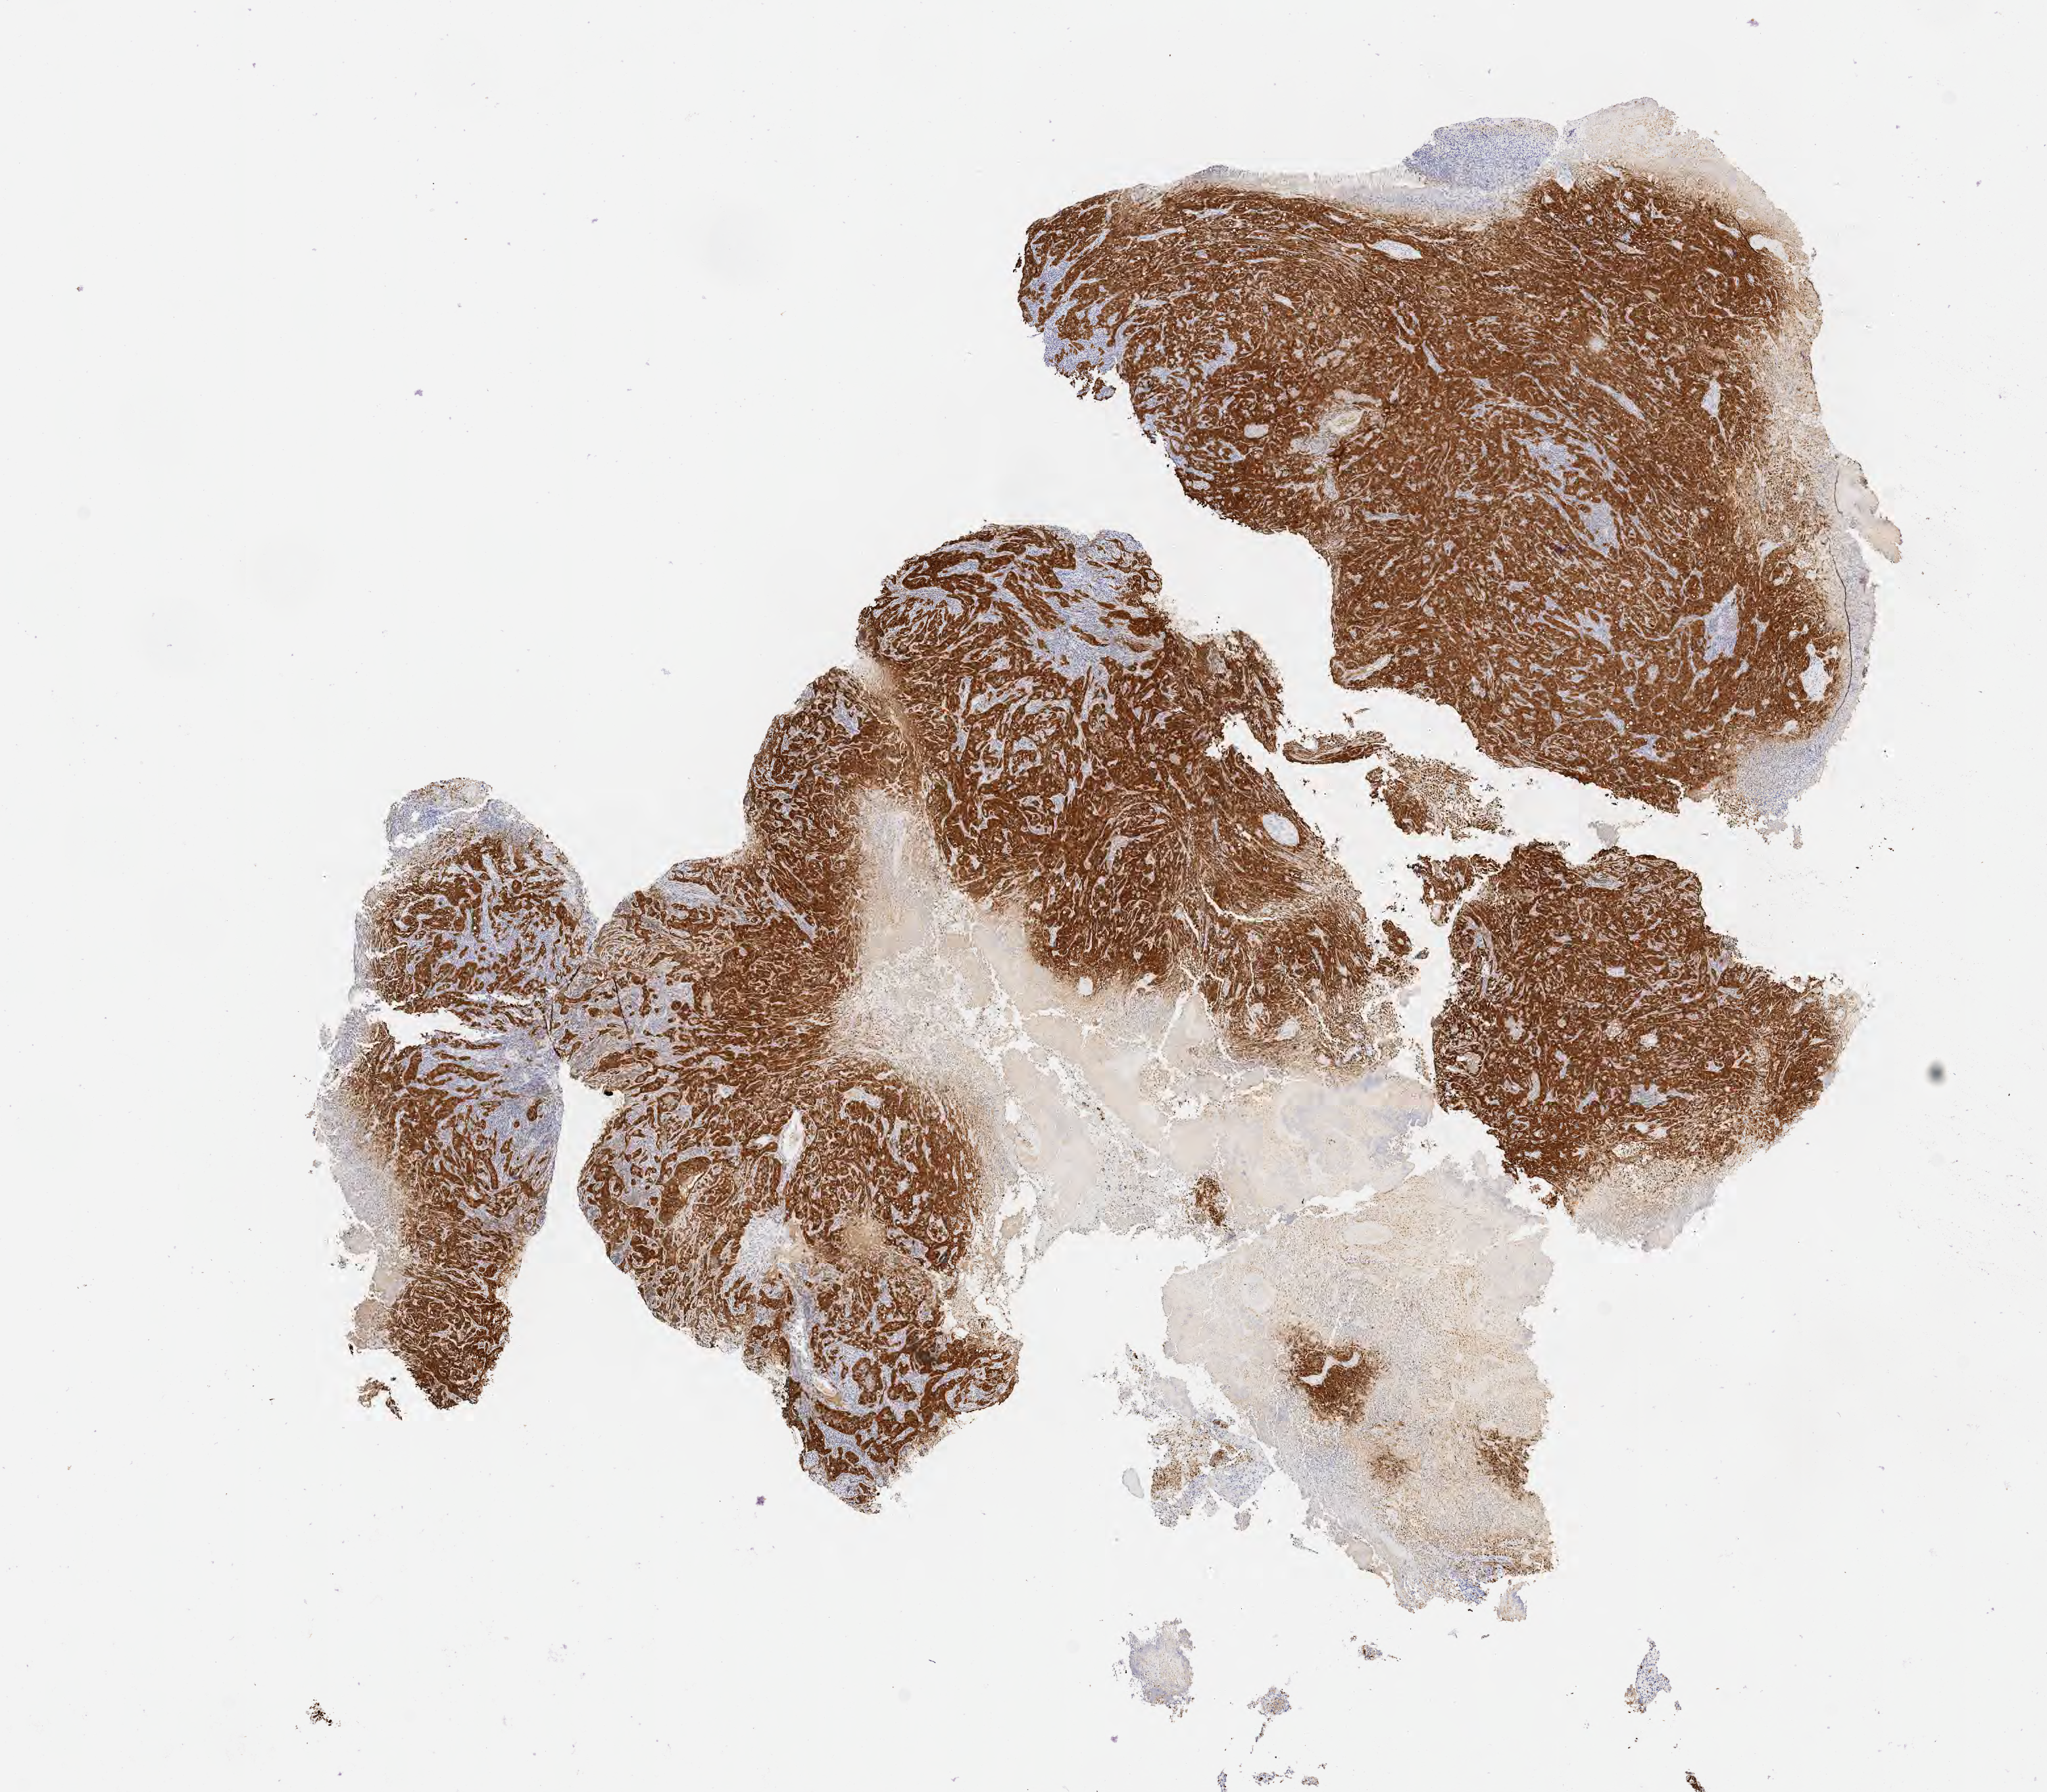
IHC for p16 (p16INK4a), whole-slide image, a low-resolution overview of the entire scanned area, about 12.6 x 11.0 mm, specimen: tumor tissue, anatomic site: cervix. Female patient, age 48 years.
* histologic diagnosis: Squamous cell carcinoma, large cell, nonkeratinizing, NOS